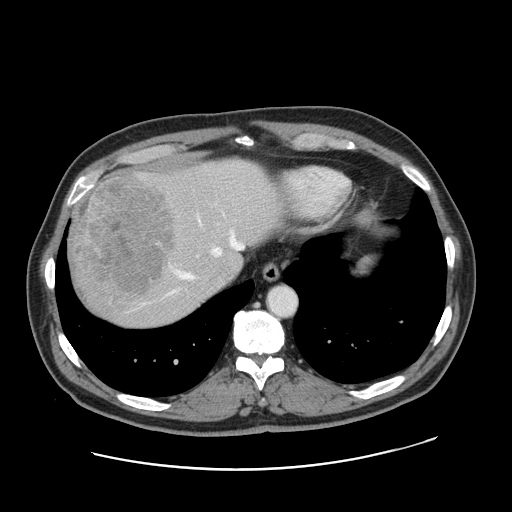
Contrast-enhanced abdominal CT, one axial slice; position 136 of 178 along the scan axis; soft-tissue window (W 400 / L 40 HU); 2.5 mm slice thickness; 512 × 512 image matrix. Male patient, age 63 years. From the clinical record (not read from this slice): diagnosis: colorectal cancer liver metastases, imaged before liver resection; multiple liver metastases: yes; largest metastasis: 8 cm; disease in both lobes: yes.
Annotated regions visible in this slice (manually delineated by an expert):
- hepatic veins: bounding box (x1, y1, x2, y2) in pixels: (169, 215, 244, 294)
- liver: (67, 158, 280, 328)
- planned liver remnant (the part of the liver to remain after resection): (170, 162, 281, 281)
- portal vein (with intrahepatic branches): (158, 242, 161, 245)
- liver metastasis: (70, 172, 175, 296)